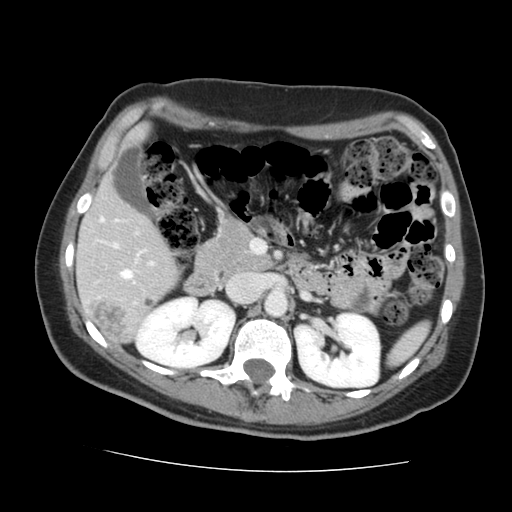
Contrast-enhanced abdominal CT, one axial slice. Position 76 of 144 along the scan axis. Intravenous contrast given. Soft-tissue window (W 400 / L 40 HU). 2.5 mm slice thickness. 512 × 512 image matrix, field of view 333 × 333 mm. Female patient, age 46 years. Case-level facts recorded for this patient, not image findings: diagnosis: colorectal cancer liver metastases, imaged before liver resection; multiple liver metastases: no.
Structures marked on this image (manually delineated by an expert):
- liver: box from (x=78, y=184) to (x=179, y=342) px
- planned liver remnant (the part of the liver to remain after resection): (x=78, y=184)–(x=179, y=335)
- portal vein (with intrahepatic branches): (x=100, y=219)–(x=153, y=279)
- liver metastasis: (x=147, y=301)–(x=153, y=306)
- liver metastasis: (x=91, y=302)–(x=129, y=341)